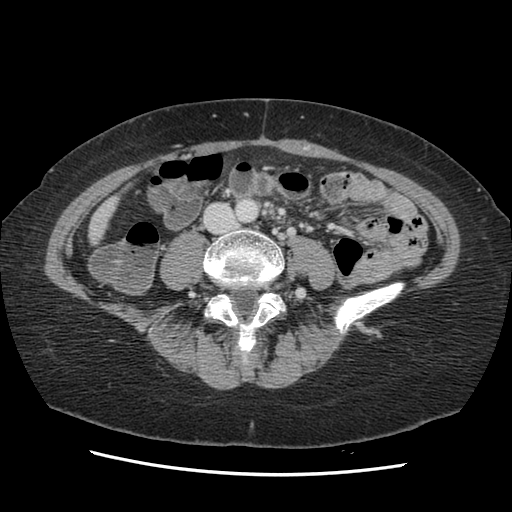
Contrast-enhanced abdominal CT, one axial slice; position 14 of 141 along the scan axis; 120 kVp; soft-tissue window (W 400 / L 40 HU); 2.5 mm slice thickness; 512 × 512 image matrix, field of view 330 × 330 mm. Female patient, age 61 years. Case-level facts recorded for this patient, not image findings: diagnosis: colorectal cancer liver metastases, imaged before liver resection; multiple liver metastases: no; largest metastasis: 2.4 cm.
Annotated regions visible in this slice (manually delineated by an expert):
- liver: bounding box <90,201,117,243> (left, top, right, bottom; pixels)
- planned liver remnant (the part of the liver to remain after resection): <90,201,116,243>